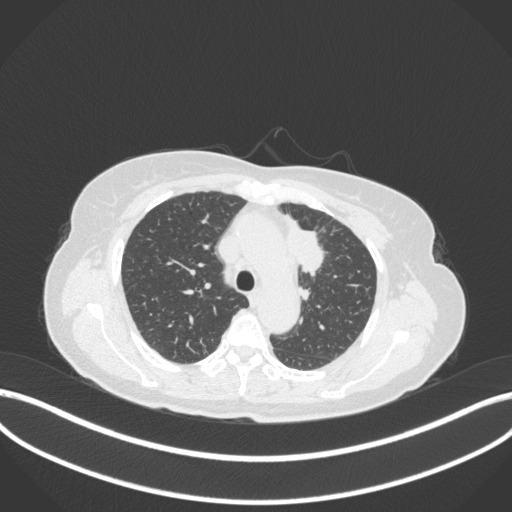
Chest CT, one axial slice; slice 240 of 368 in the series (ordered by position); reconstruction kernel B31f; 120 kVp; lung window (W 1500 / L -600 HU); 1 mm slice thickness; 512 × 512 image matrix, field of view 400 × 400 mm. Patient: female, 65 years. From the clinical record (not read from this slice): clinical TNM (as recorded): T2a N0 M0; histopathological grade: G2-3.
Structures marked on this image (bounding box drawn by a radiologist):
- lung tumour (recorded histology: adenocarcinoma): box from (x=283, y=216) to (x=328, y=276) px